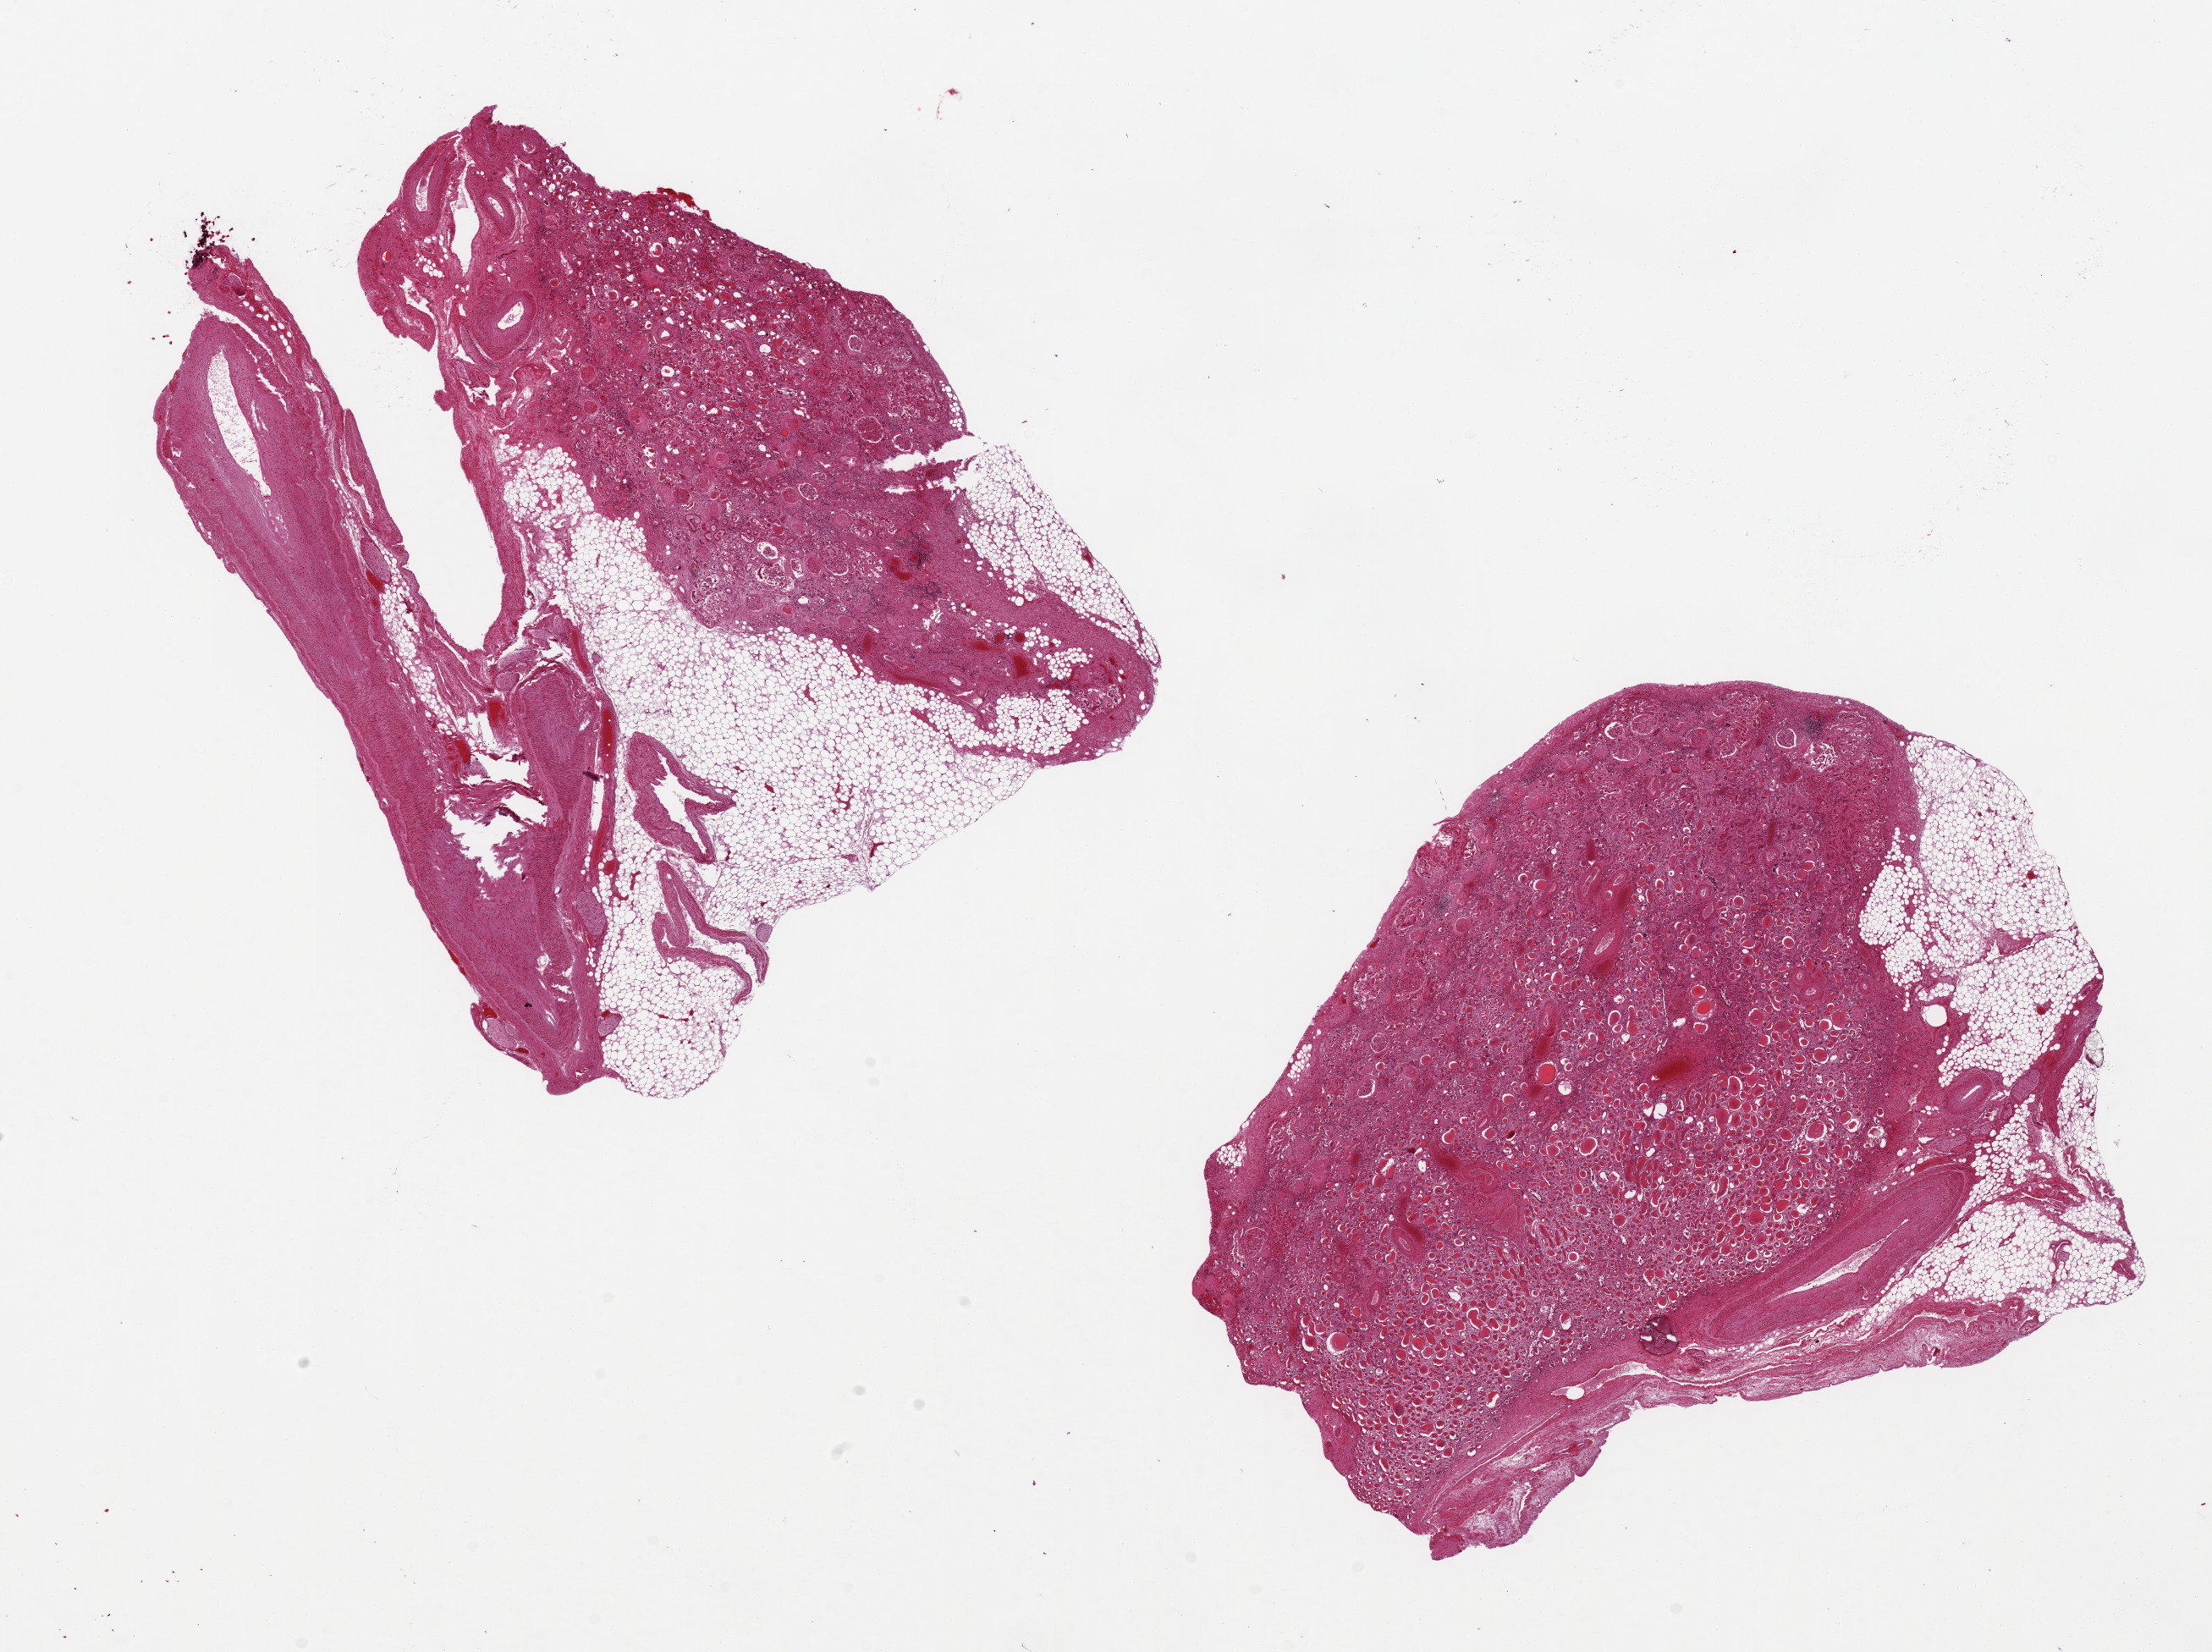
Whole-slide image, H&E stain, brightfield — whole scanned area (about 20.7 x 15.4 mm) shown as a low-resolution overview; PAXgene-fixed paraffin-embedded (PFPE) section; target tissue: renal medulla; donor tissue sample. Donor: male.
Reviewer comment on this tissue sample: 2 pieces, 50% fat an/or cortex with end-stage chronic fibrosing glomerulonepritis.